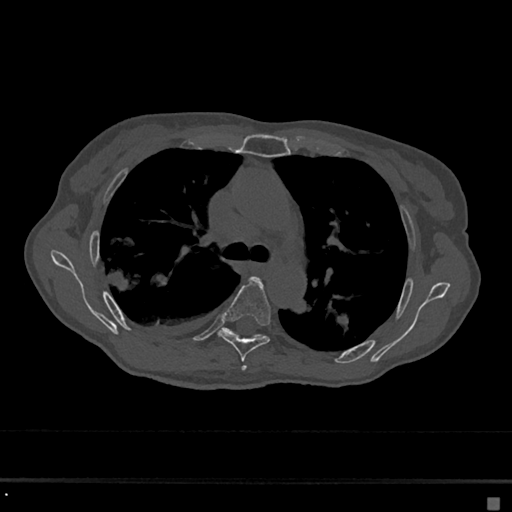
CT including the spine, one axial slice. Slice 456 of 797 in the series (ordered by position). Reconstruction kernel Br40s/3. Bone window (W 1800 / L 400 HU). 0.5 mm slice thickness. 512 × 512 image matrix, field of view 360 × 360 mm. Female patient, age 68 years. Case-level facts recorded for this patient, not image findings: primary cancer: renal.
Annotated regions visible in this slice (semi-automatically segmented with operator editing):
- T4 vertebra: bounding box <242,365,247,371> (left, top, right, bottom; pixels)
- T5 vertebra: <218,278,271,362>
- T6 vertebra: <223,328,264,339>